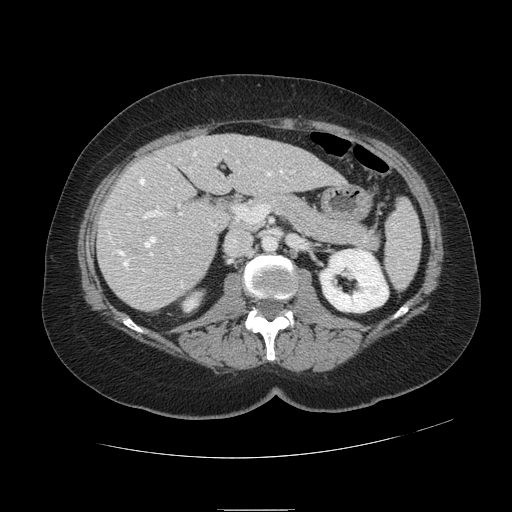
Contrast-enhanced abdominal CT, one axial slice. Position 47 of 121 along the scan axis. 120 kVp. Intravenous contrast given. Soft-tissue window (W 400 / L 40 HU). 2.5 mm slice thickness. 512 × 512 image matrix, field of view 400 × 400 mm. Female patient, age 52 years. From the clinical record (not read from this slice): diagnosis: colorectal cancer liver metastases, imaged before liver resection; multiple liver metastases: yes; largest metastasis: 6.3 cm; chemotherapy before resection: yes.
Outlined on this slice (outlined manually by an expert reader):
- hepatic veins: box from (x=109, y=150) to (x=283, y=287) px
- liver: (x=97, y=135)–(x=342, y=311)
- planned liver remnant (the part of the liver to remain after resection): (x=174, y=135)–(x=343, y=195)
- portal vein (with intrahepatic branches): (x=128, y=161)–(x=239, y=271)